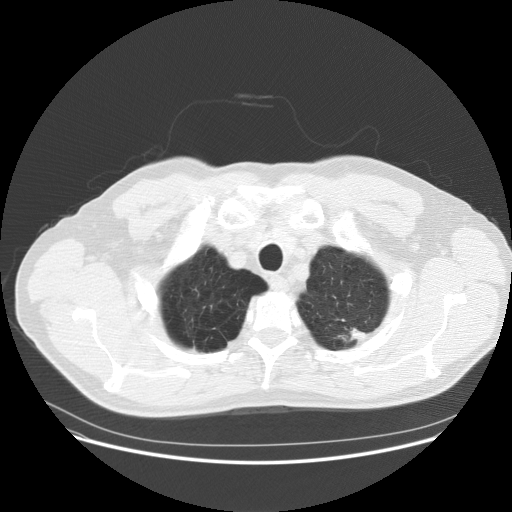
Low-dose screening chest CT, one axial slice; position 147 of 158 along the scan axis; 120 kVp; lung window (W 1500 / L -600 HU); 2.5 mm slice thickness; 512 × 512 image matrix, field of view 400 × 400 mm.
Annotated regions visible in this slice (expert manual segmentation):
- lesion 1 (tumor, upper lobe of left lung): bounding box [x1, y1, x2, y2] px = [350, 328, 368, 343]